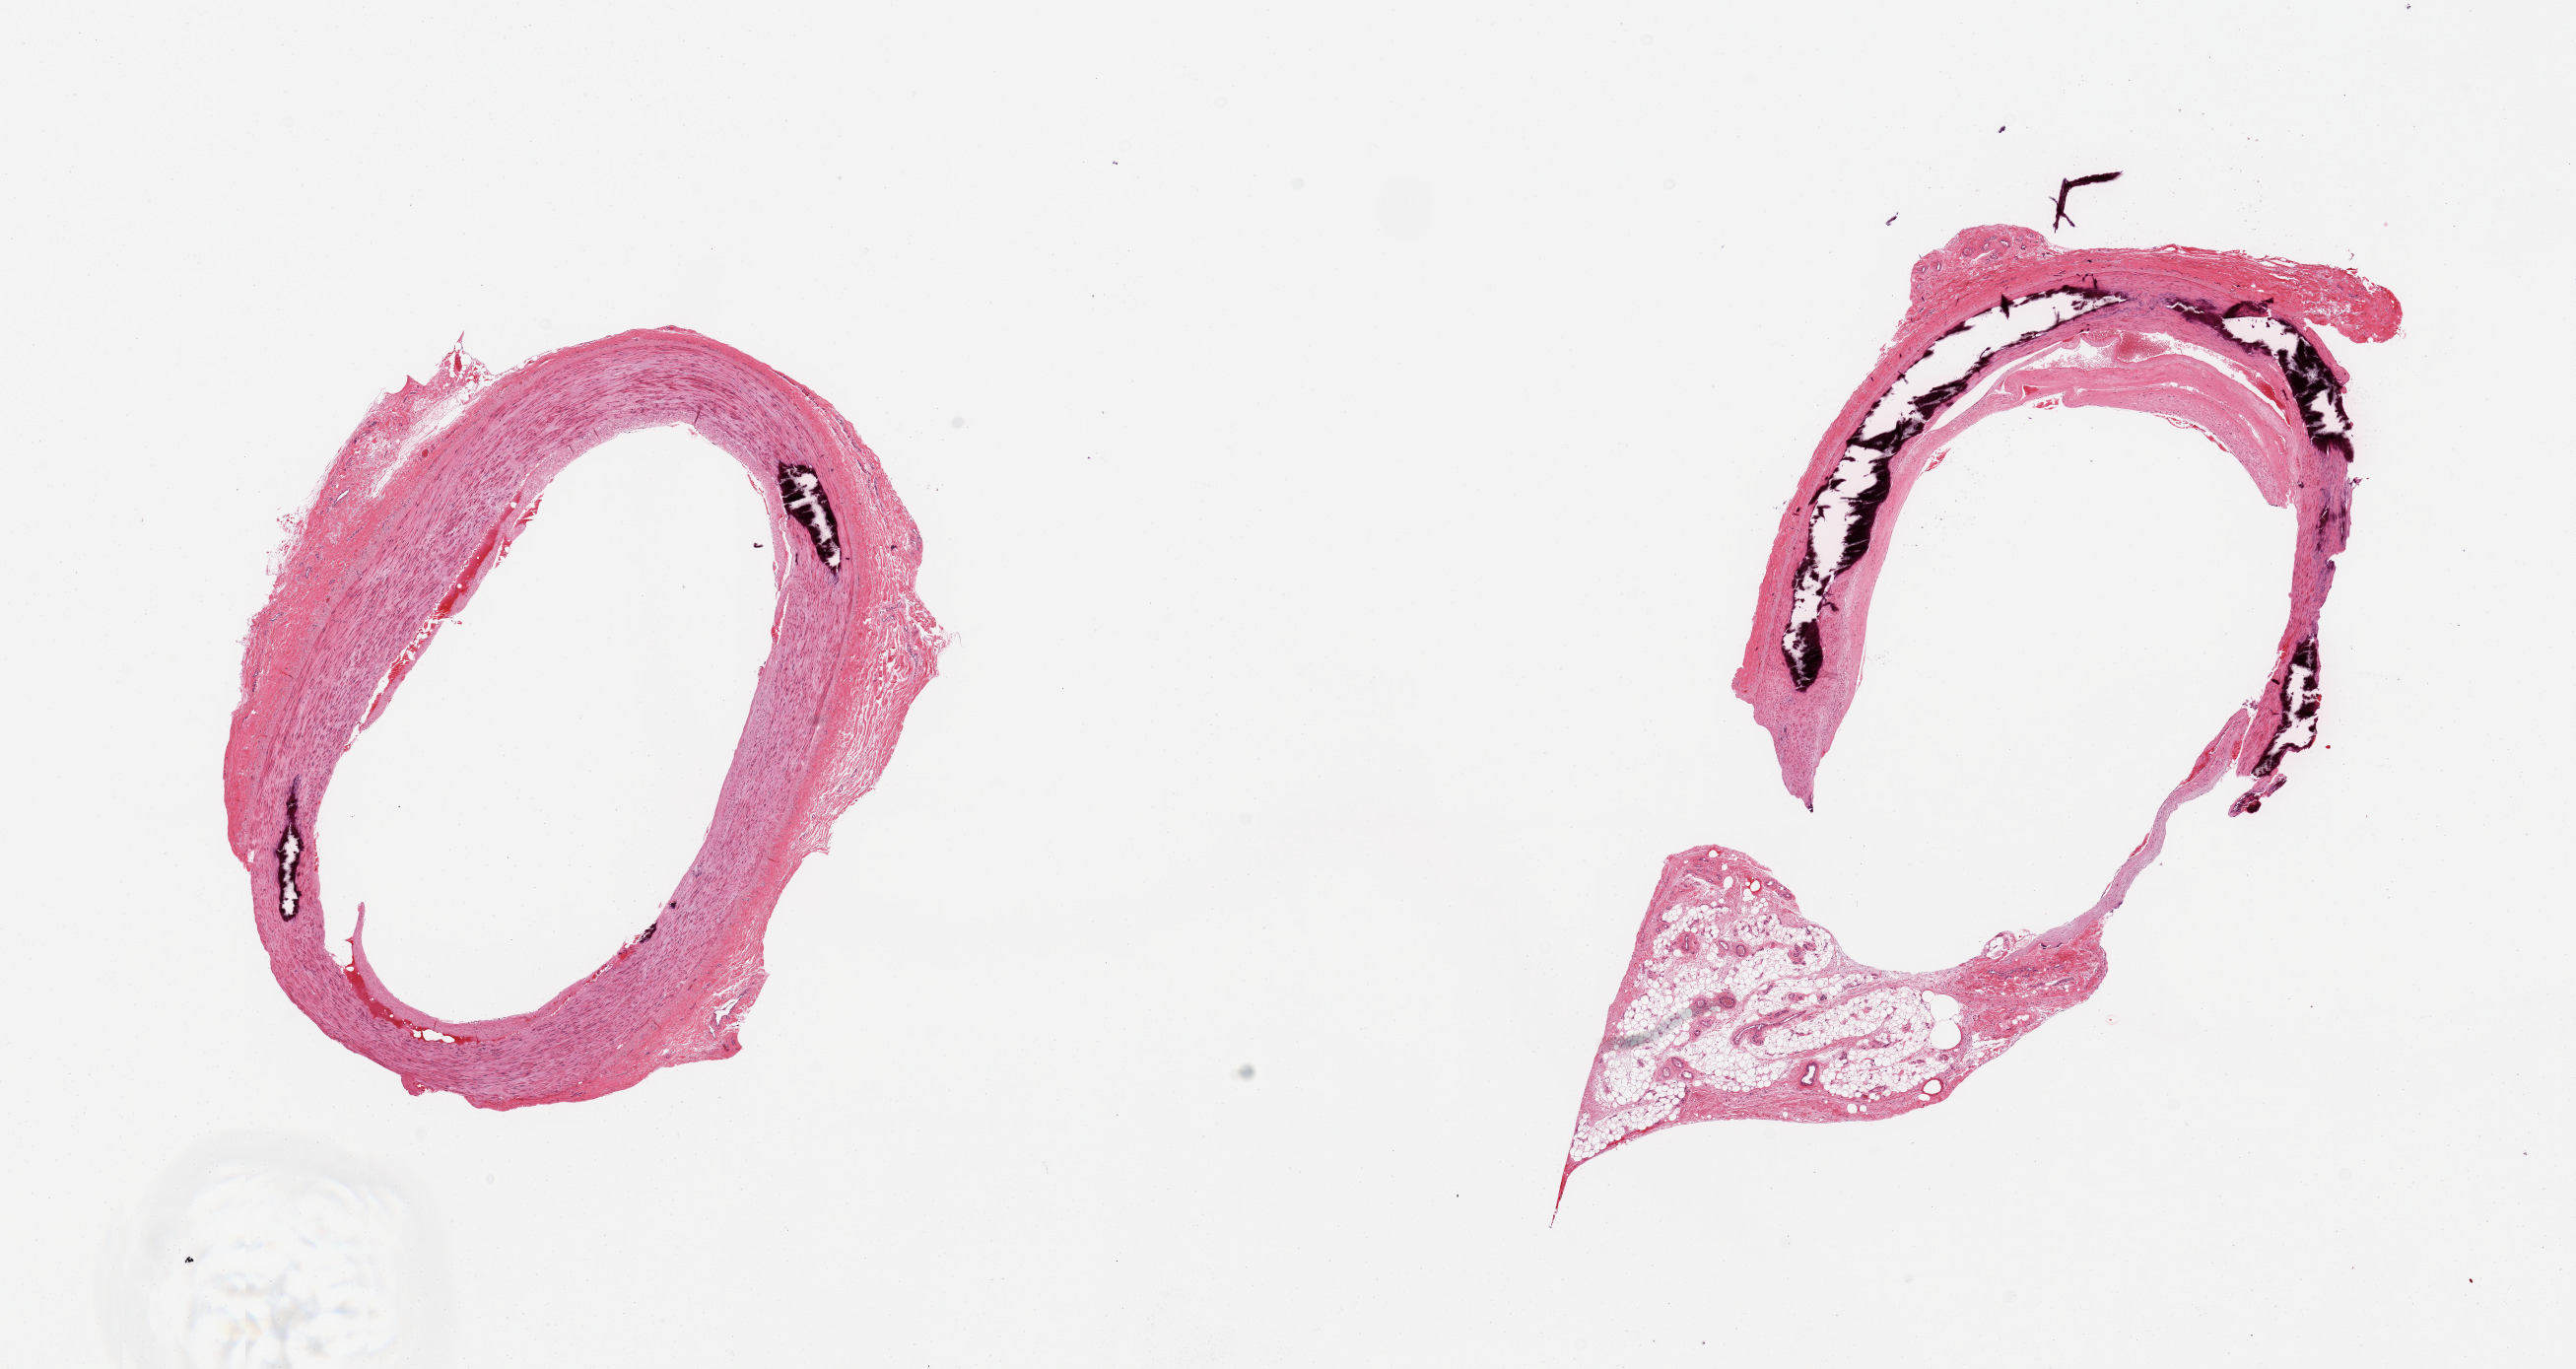
Digitized haematoxylin and eosin-stained section, brightfield, shown as a low-resolution overview of the whole scanned area (about 20.7 x 11.0 mm), PAXgene-fixed, paraffin-embedded tissue, sampled site (target tissue): tibial artery, tissue donor sample. Donor: female.
- review note (as recorded): 2 pieces; 1 piece heavily [50%] calcified, other focally; fatty external 'tail' on 1 piece